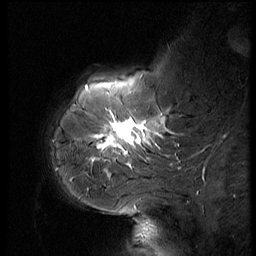
Breast MRI (dynamic contrast-enhanced), one sagittal slice. Slice 14 of 56 in the series (ordered by position). Dynamic contrast-enhanced series, image 2 of 3 at this slice position (ordered by acquisition). 1.5 T. TE 4.2 ms, TR 9 ms. 2.5 mm slice thickness. 256 × 256 image matrix. Female patient, age 61 years. From the clinical record (not read from this slice): setting: breast cancer imaged before/during neoadjuvant chemotherapy; receptor status: HR-positive, HER2-negative.
Outlined on this slice (semi-automatically segmented with operator editing):
- analysis volume of interest (the breast-tissue region the enhancement analysis was run in; not a lesion): box from (x=65, y=74) to (x=185, y=175) px
- tumour enhancement mask (voxels above the 140 % enhancement threshold inside the analysis volume of interest): (x=93, y=109)–(x=163, y=169)